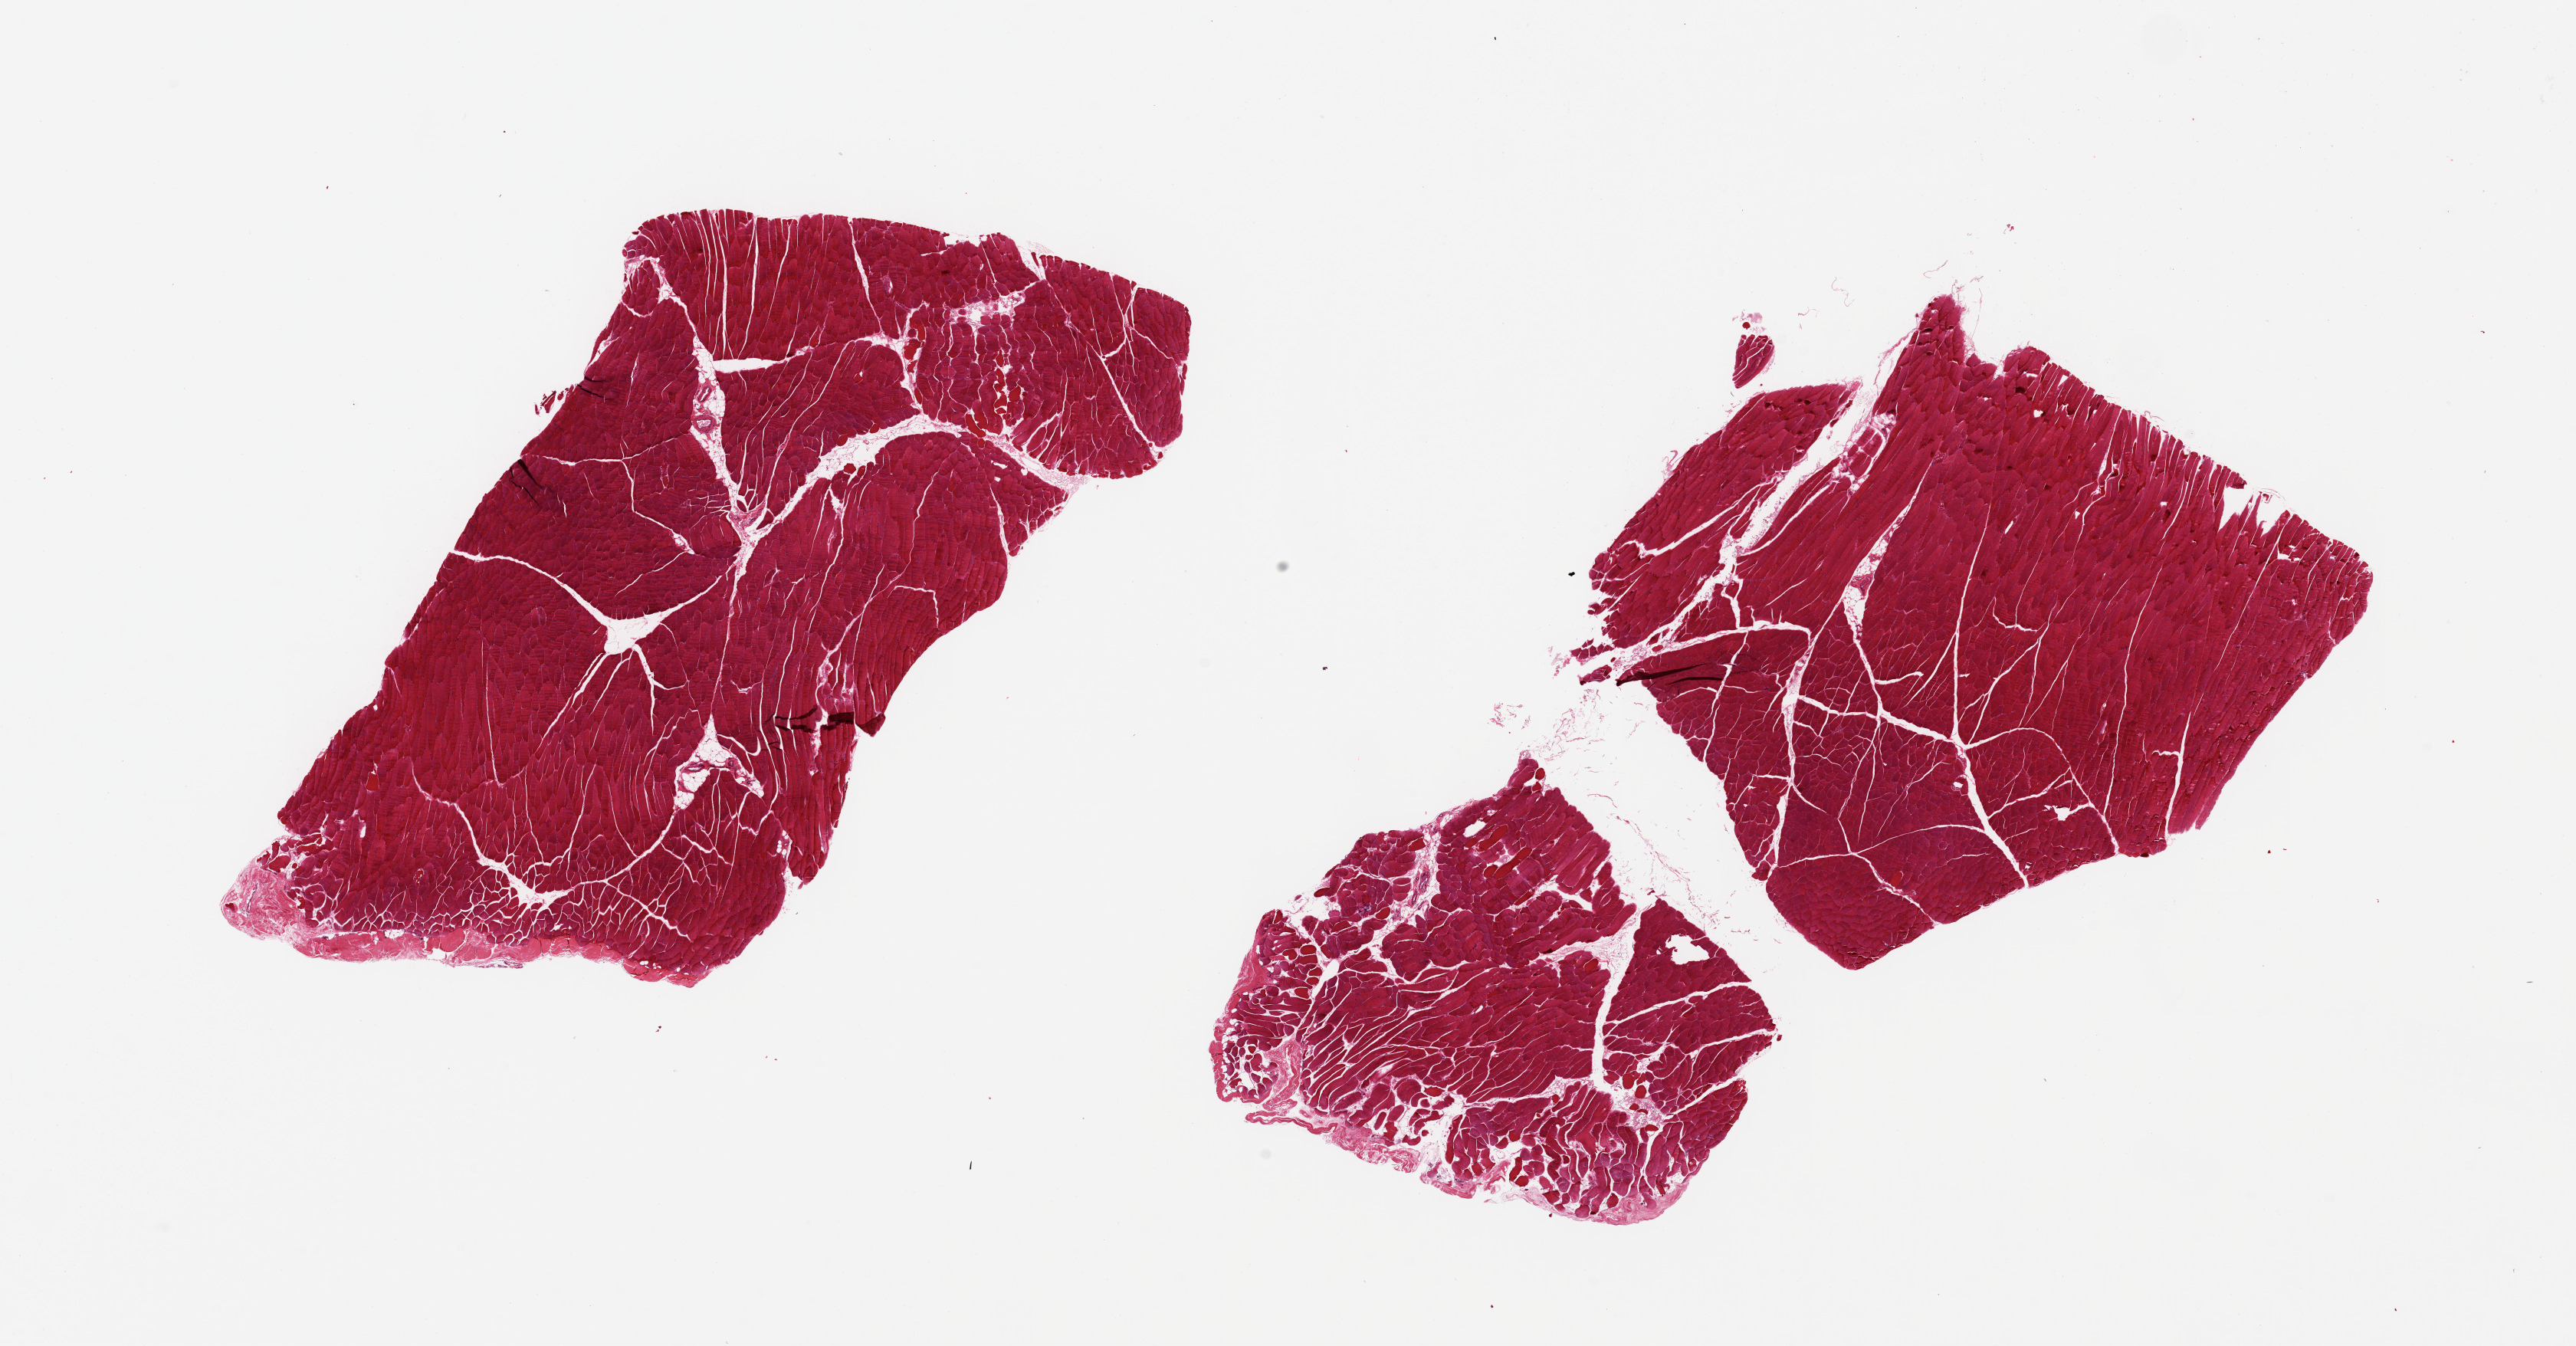
Whole-slide image, H&E stain — a low-resolution overview of the entire scanned area, about 26.6 x 13.9 mm. PAXgene-fixed paraffin-embedded (PFPE) section. Sampled site (target tissue): skeletal muscle. Tissue donor sample. Donor: male.
Reviewer comment on this tissue sample: 2 pieces, 9x6 & 11.5x7mm; Contraction bands.